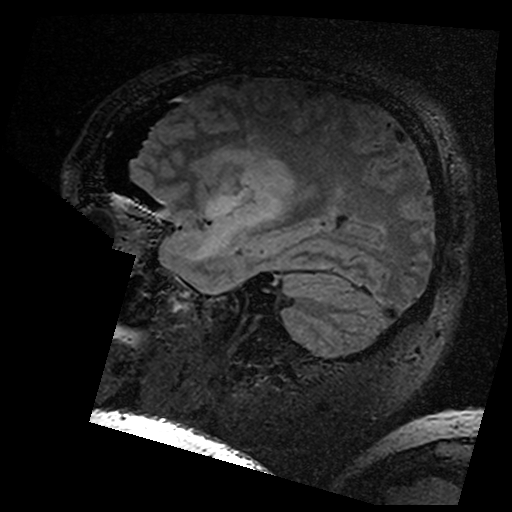
Brain MRI from a brain-tumour surgery series, one sagittal slice. Position 120 of 176 along the scan axis. T2 FLAIR. 1 mm slice thickness. 512 × 512 image matrix, field of view 250 × 250 mm. Case-level facts recorded for this patient, not image findings: histopathology: Astrocytoma; WHO grade: 3; IDH mutation: yes.
Outlined on this slice (expert manual segmentation):
- residual tumour: bounding box [x1, y1, x2, y2] px = [202, 145, 292, 197]